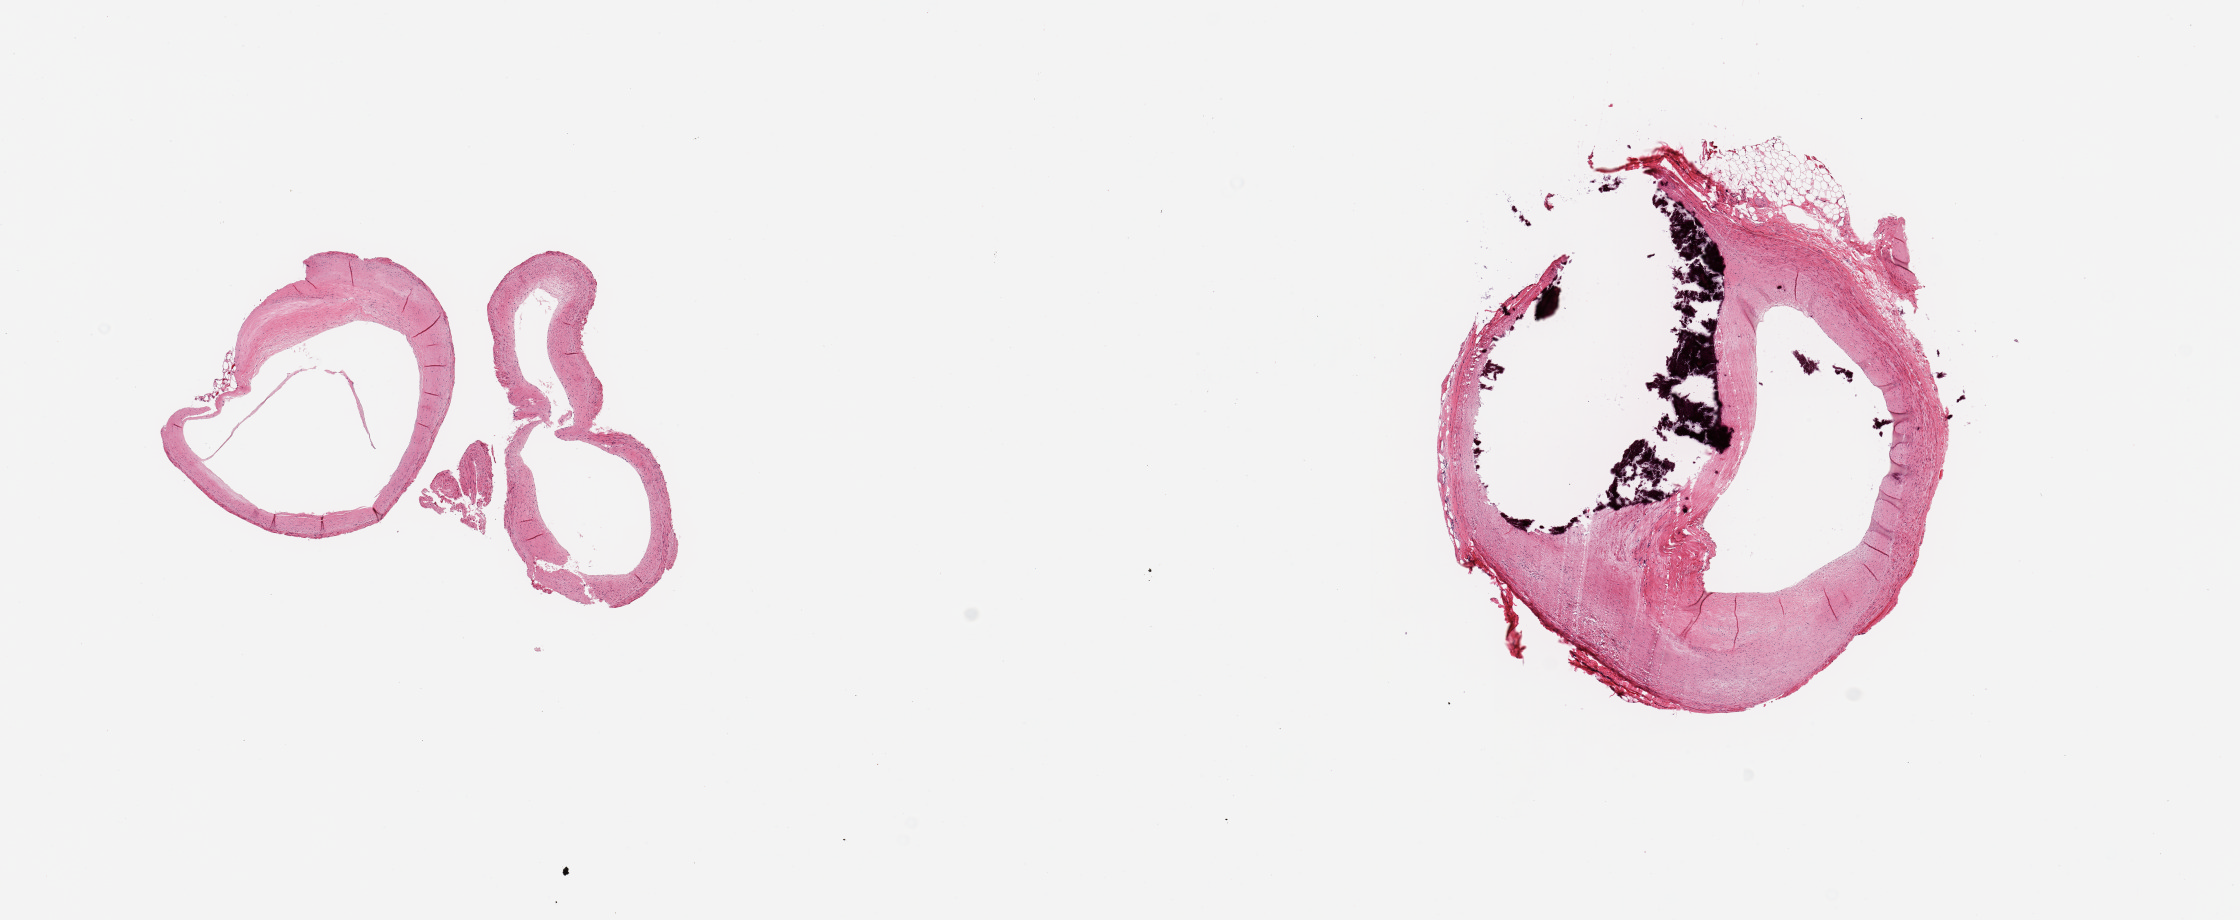
Whole-slide image, hematoxylin and eosin (H&E) stain — low-resolution overview of the scanned area, about 17.7 x 7.3 mm (slide scanned at 20x). PAXgene-fixed, paraffin-embedded tissue. Target tissue: coronary artery. Tissue donor sample.
Review note (as recorded): 2 pieces 20-50% occlusive atherosis, focally calicified.